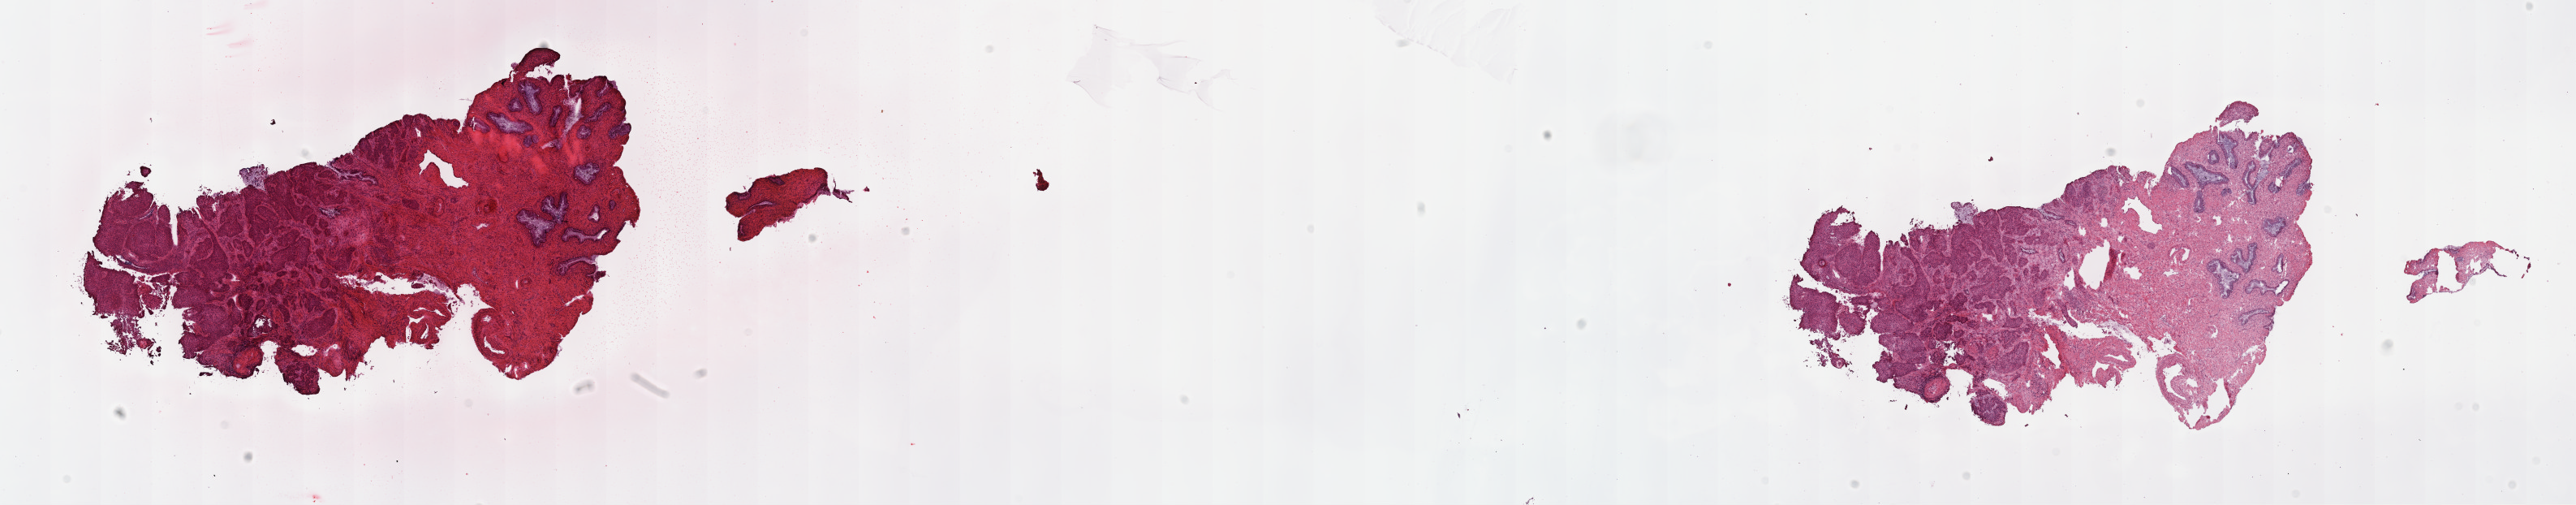
H&E whole-slide image — low-resolution overview of the scanned area, about 25.7 x 5.0 mm. Frozen section from the top of the tissue portion. Primary tumour sample from the cervix. Female patient; age at initial diagnosis 26 years. Histologic grade: G2 (moderately differentiated). Pathologist review of this section (percent, as recorded): tumour cells 60%, tumour nuclei 60%, normal cells 0%, stromal cells 40%, necrosis 0%. Inflammatory infiltration, as recorded: lymphocyte infiltration 0%, monocyte infiltration 0%, neutrophil infiltration 0%.
FIGO stage: IB1. Histologic diagnosis: Squamous cell carcinoma, NOS. Lymph nodes positive (case pathology): 0 of 42 examined.